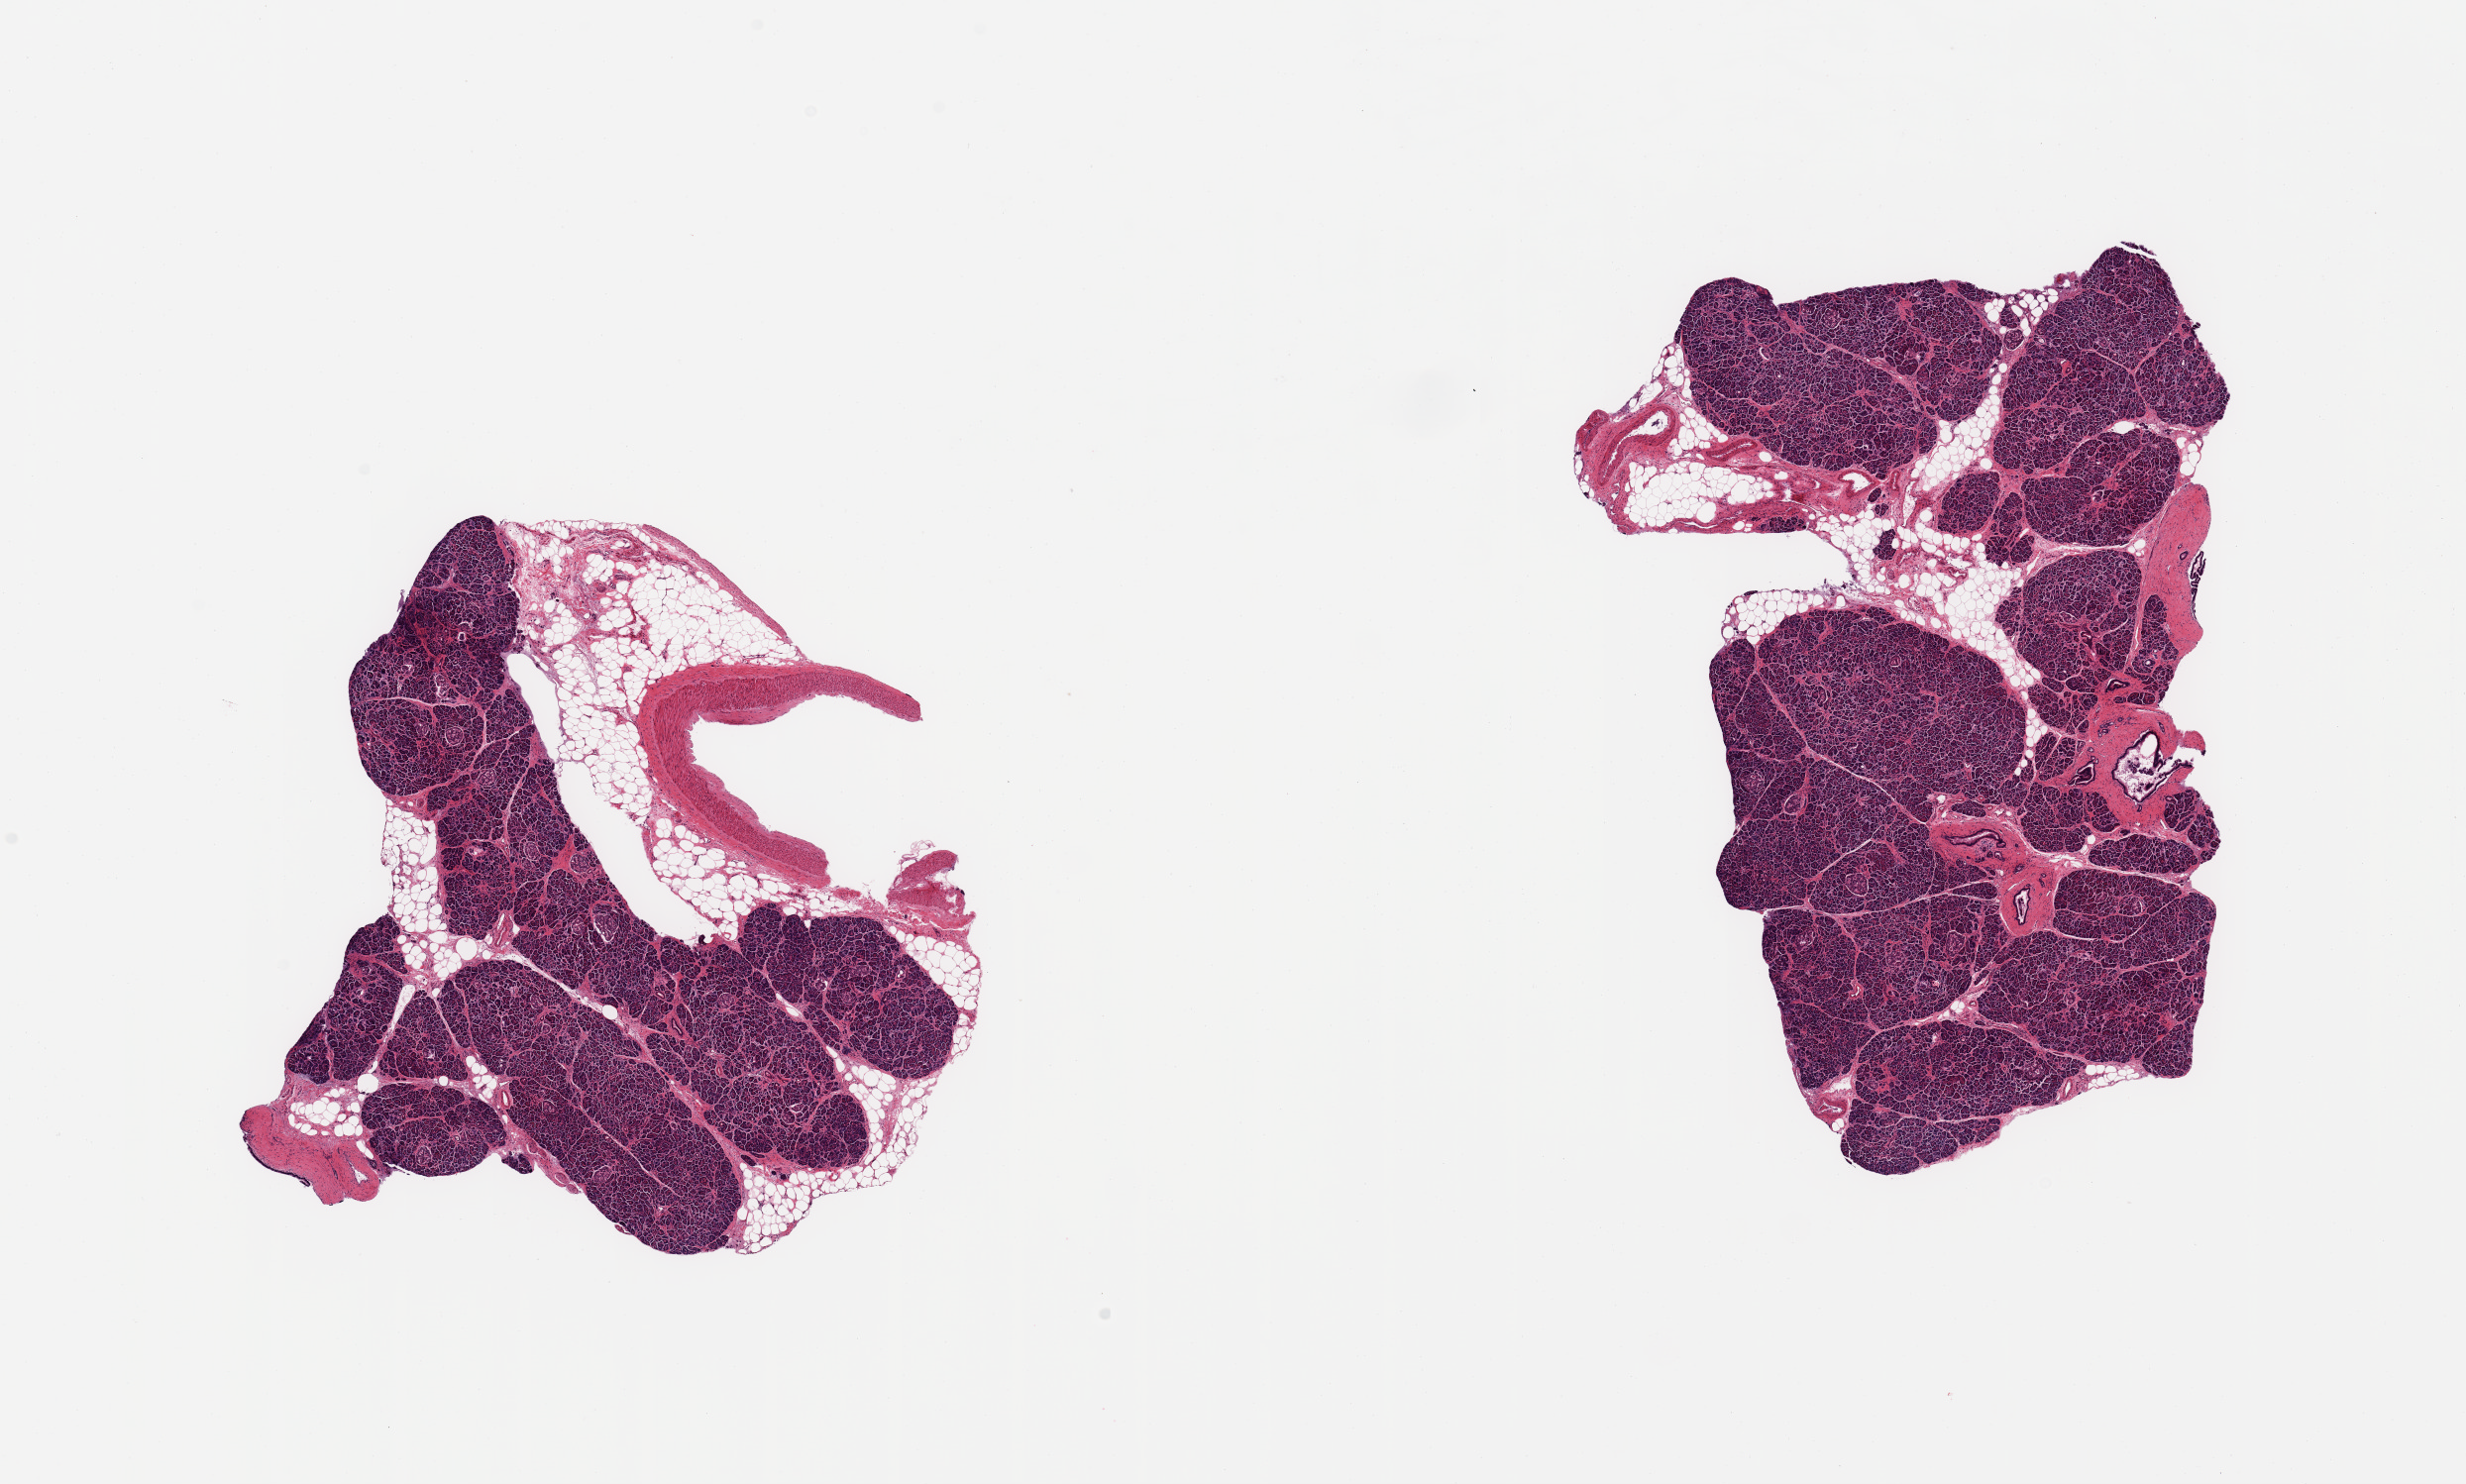
Whole-slide image, haematoxylin and eosin stain, brightfield, low-resolution overview of the scanned area, about 19.7 x 11.8 mm; PAXgene-fixed paraffin-embedded (PFPE) section; target tissue: pancreas; donor tissue sample. Donor sex: male.
Review note (as recorded): 2 pieces; well preserved parenchyma and Langerhans islets; ~20% and 10% attached fat.